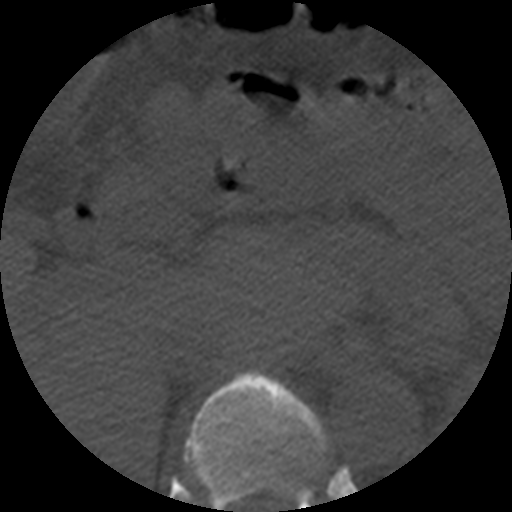
CT including the spine, one axial slice; position 252 of 508 along the scan axis; reconstruction kernel STANDARD; bone window (W 1800 / L 400 HU); 1.25 mm slice thickness; 512 × 512 image matrix, field of view 160 × 160 mm. Patient age 57 years. Case-level facts recorded for this patient, not image findings: primary cancer: prostate.
Structures marked on this image (semi-automatically segmented with operator editing):
- T11 vertebra: bounding box <184,371,328,512> (left, top, right, bottom; pixels)